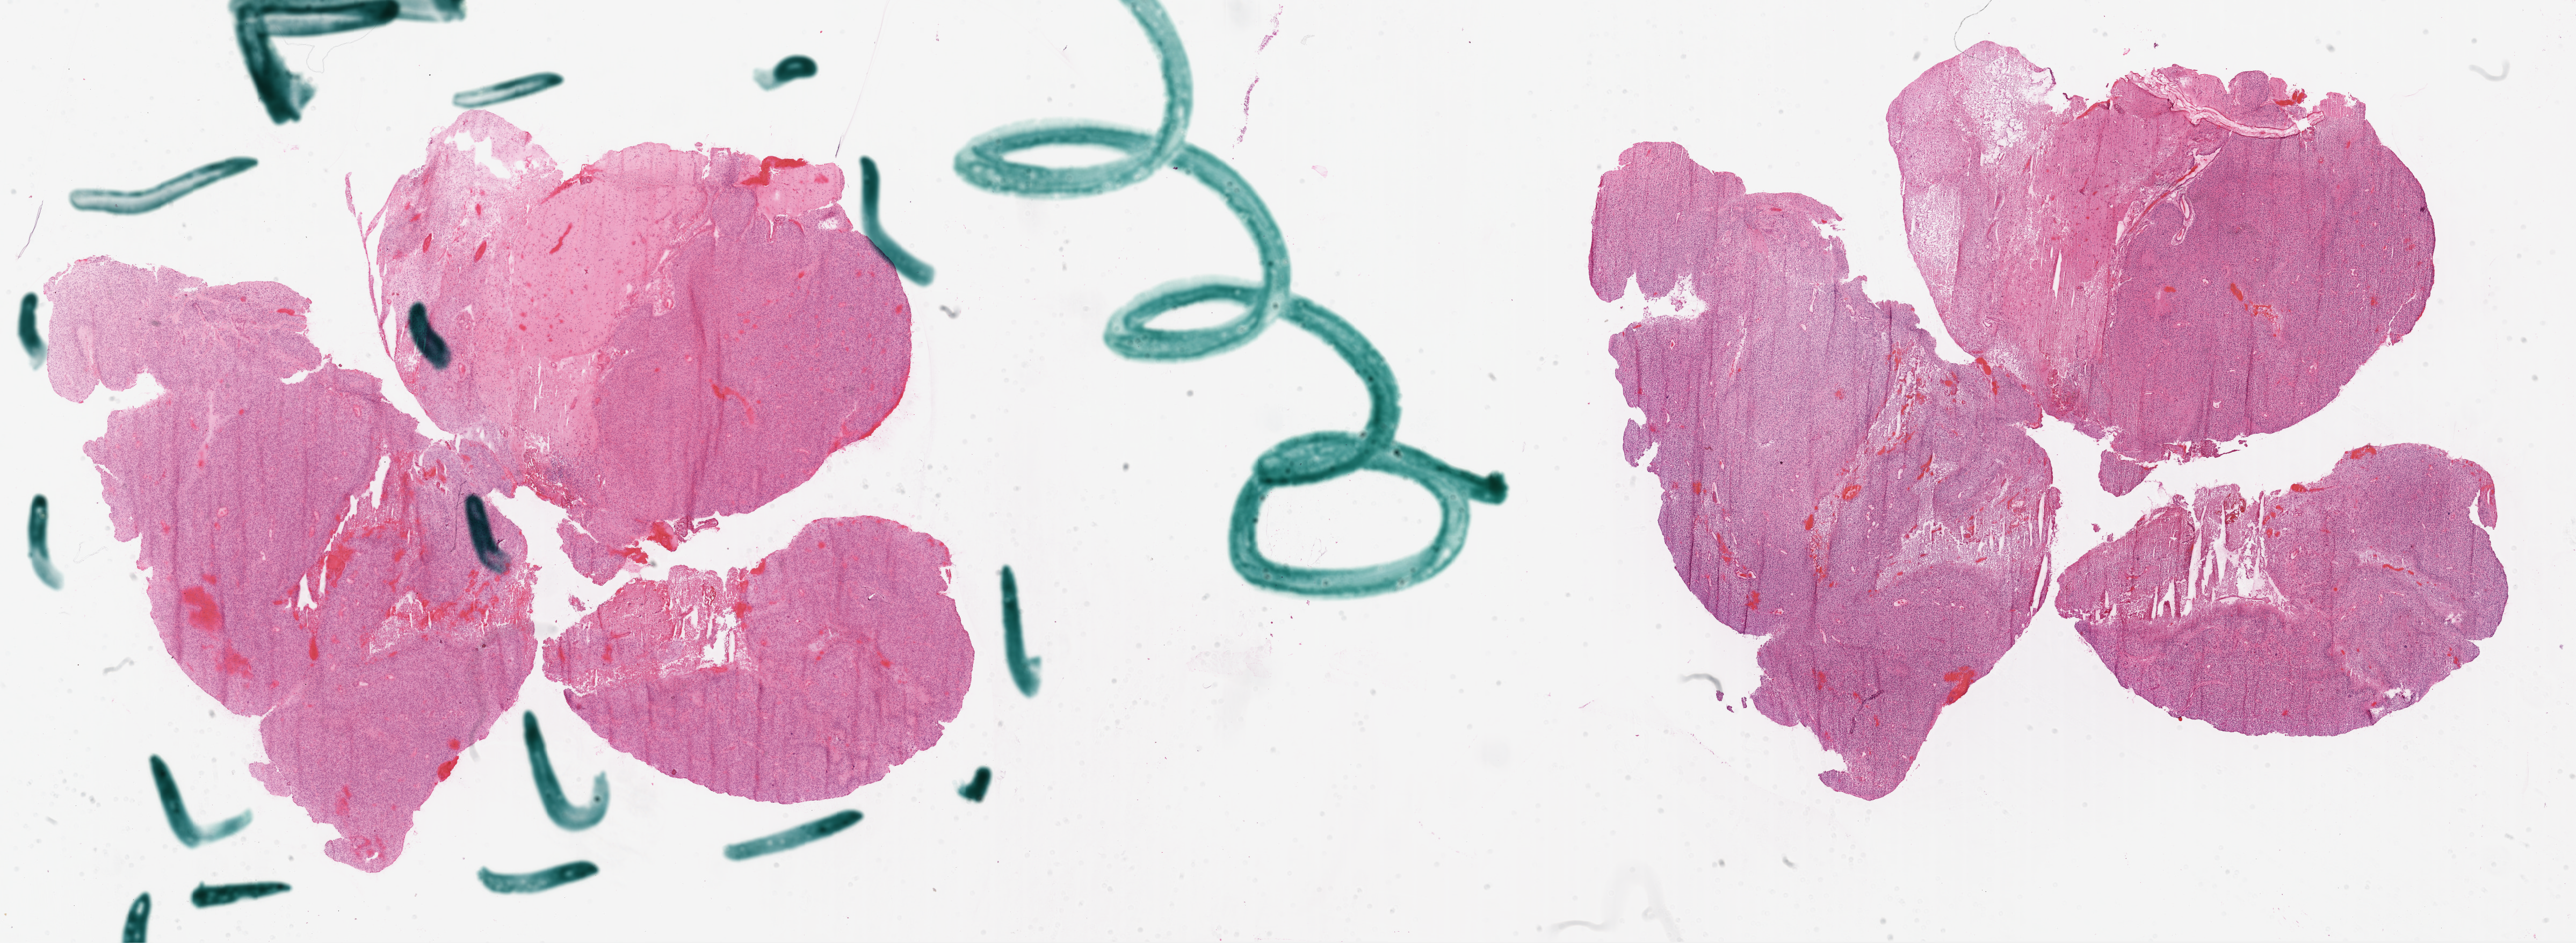
H&E whole-slide image, a low-resolution overview of the entire scanned area, about 38.7 x 14.2 mm (from a 20x scan), frozen section from the top of the tissue portion, sample: primary tumour, brain. Male, age 42 years at initial diagnosis.
Histologic diagnosis: Glioblastoma.